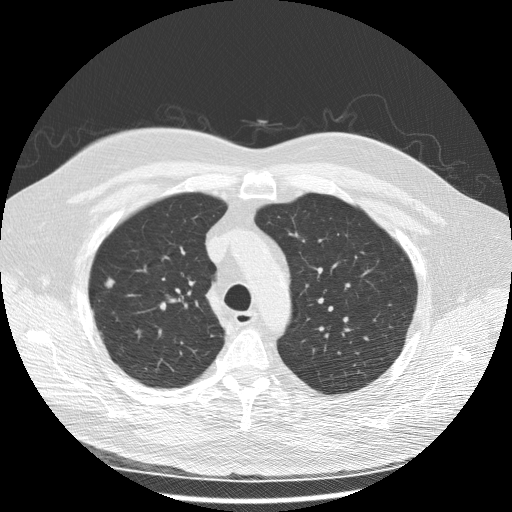
Low-dose screening chest CT, one axial slice. Lung window (W 1500 / L -600 HU). 2.5 mm slice thickness. 512 × 512 image matrix, field of view 380 × 380 mm.
Structures marked on this image (manually delineated by an expert):
- lesion 1 (tumor, upper lobe of right lung): box from (x=105, y=277) to (x=115, y=288) px